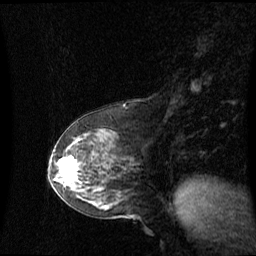
Breast MRI (dynamic contrast-enhanced), one sagittal slice. Slice 31 of 60 in the series (ordered by position). Dynamic contrast-enhanced series, image 2 of 3 at this slice position (ordered by acquisition). 1.5 T. TE 4.2 ms, TR 8.4 ms. 2.1 mm slice thickness. 256 × 256 image matrix, field of view 260 × 260 mm. Patient: female, 59 years. From the clinical record (not read from this slice): setting: breast cancer imaged before/during neoadjuvant chemotherapy; receptor status: HR-positive, HER2-negative.
Structures marked on this image (semi-automatically segmented with operator editing):
- analysis volume of interest (the breast-tissue region the enhancement analysis was run in; not a lesion): box from (x=55, y=148) to (x=87, y=191) px
- tumour enhancement mask (voxels above the 70 % enhancement threshold inside the analysis volume of interest): (x=61, y=162)–(x=79, y=179)